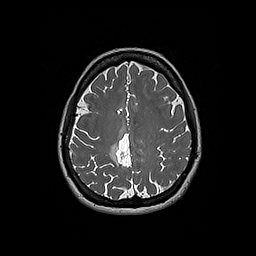
Brain MRI from a brain-tumour surgery series, one axial slice. Position 64 of 192 along the scan axis. 256 × 256 image matrix. Case-level facts recorded for this patient, not image findings: histopathology: Oligodendroglioma; WHO grade: 2; IDH mutation: yes.
Outlined on this slice (outlined manually by an expert reader):
- tumour: box from (x=110, y=143) to (x=119, y=166) px